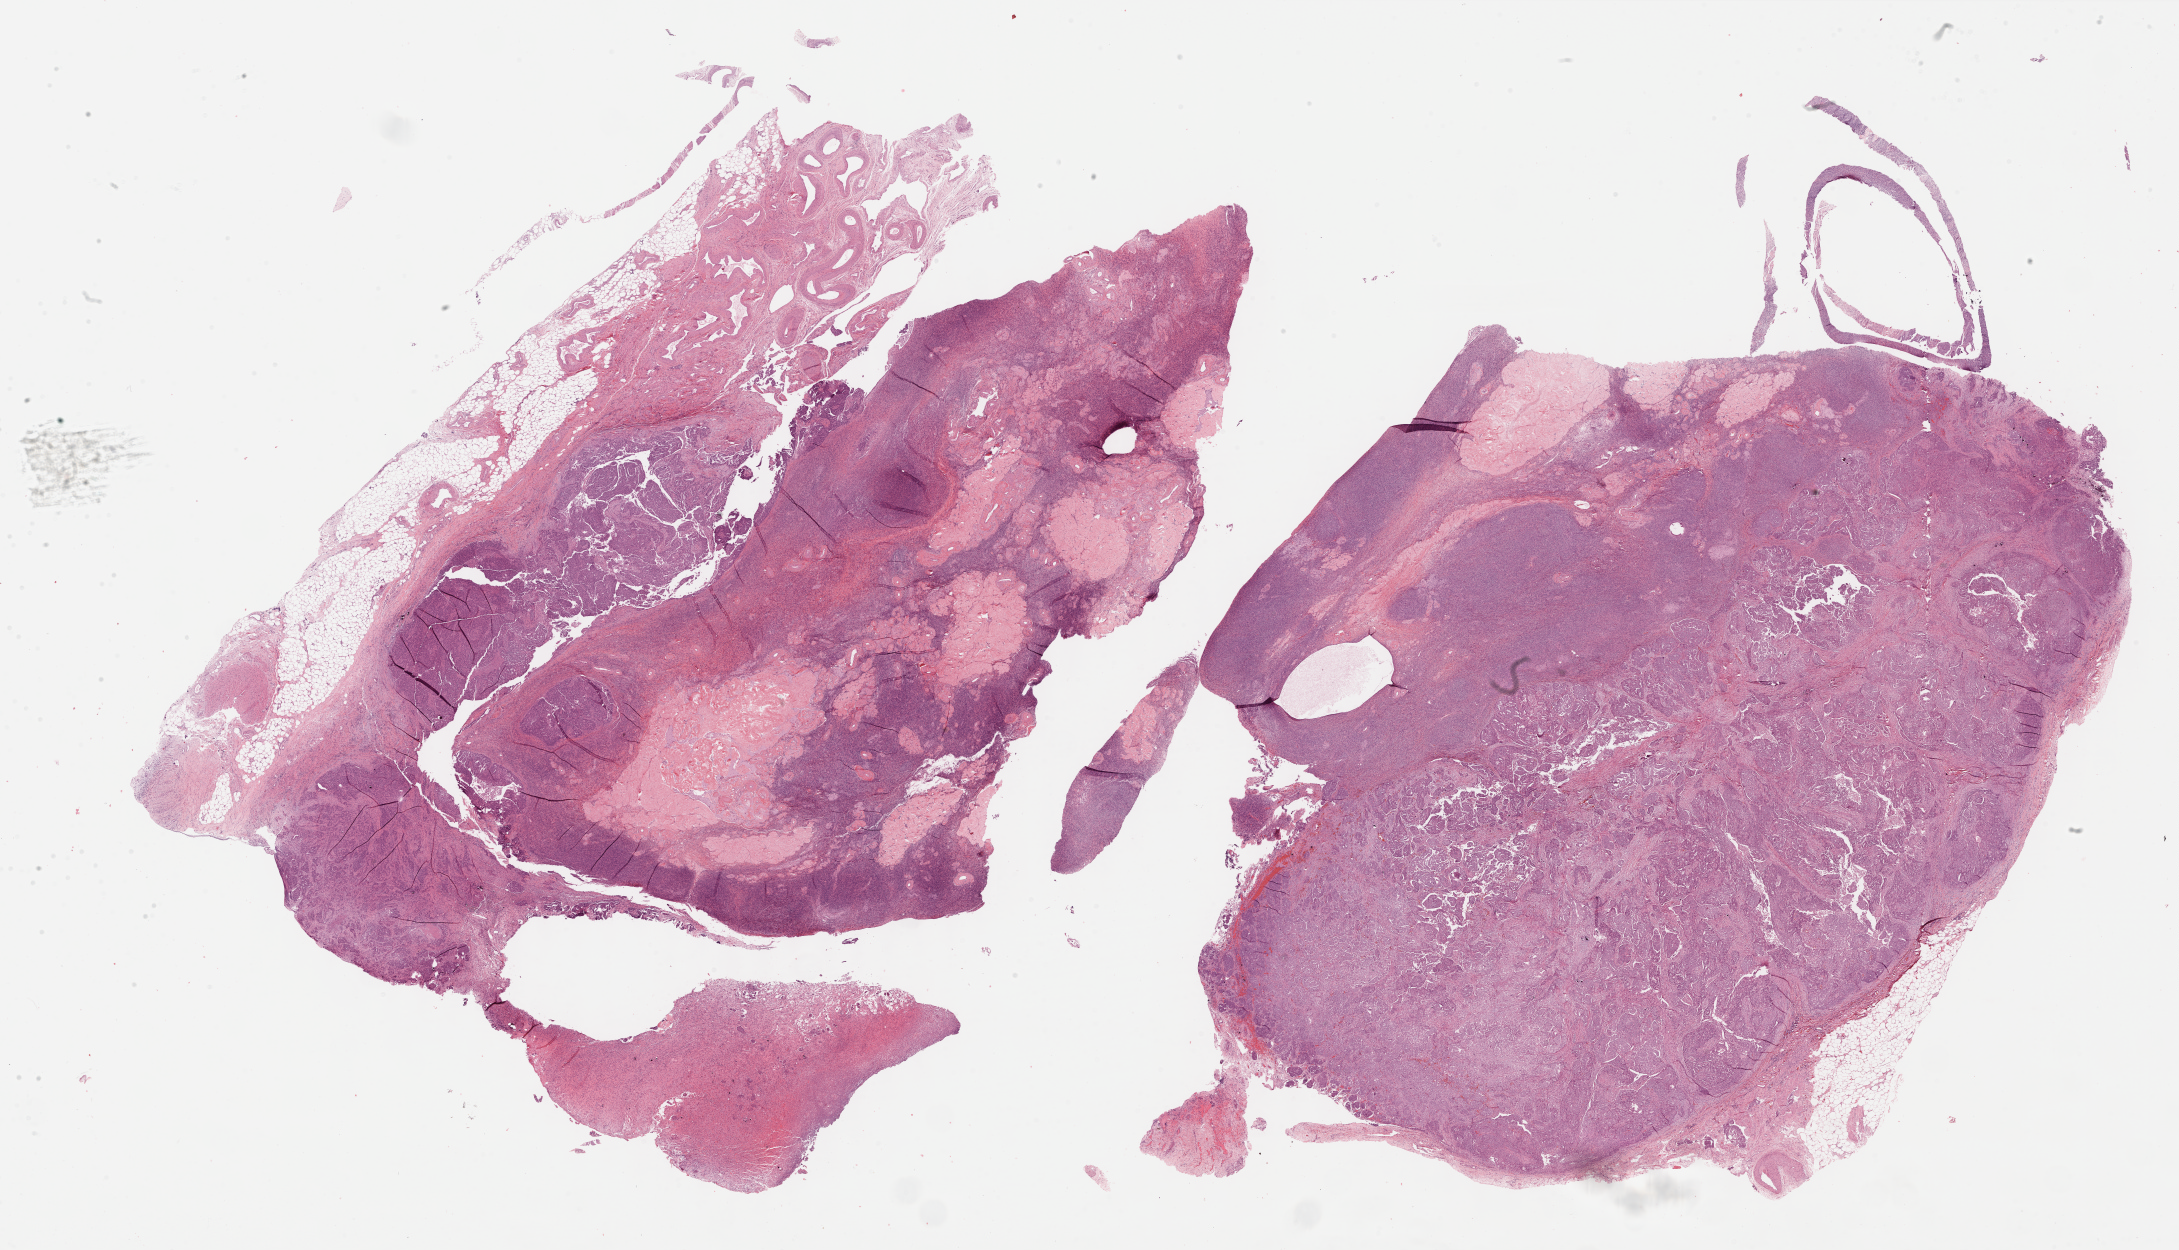
Whole-slide histology image, H&E — low-resolution overview of the scanned area, about 35.2 x 20.2 mm. Formalin-fixed paraffin-embedded (FFPE) diagnostic section. Primary tumour sample from the ovary. Female patient; age at initial diagnosis 80 years. Histologic grade: G3 (poorly differentiated).
FIGO stage: IIIC. Laterality: bilateral. Pathologic diagnosis: Serous cystadenocarcinoma, NOS.